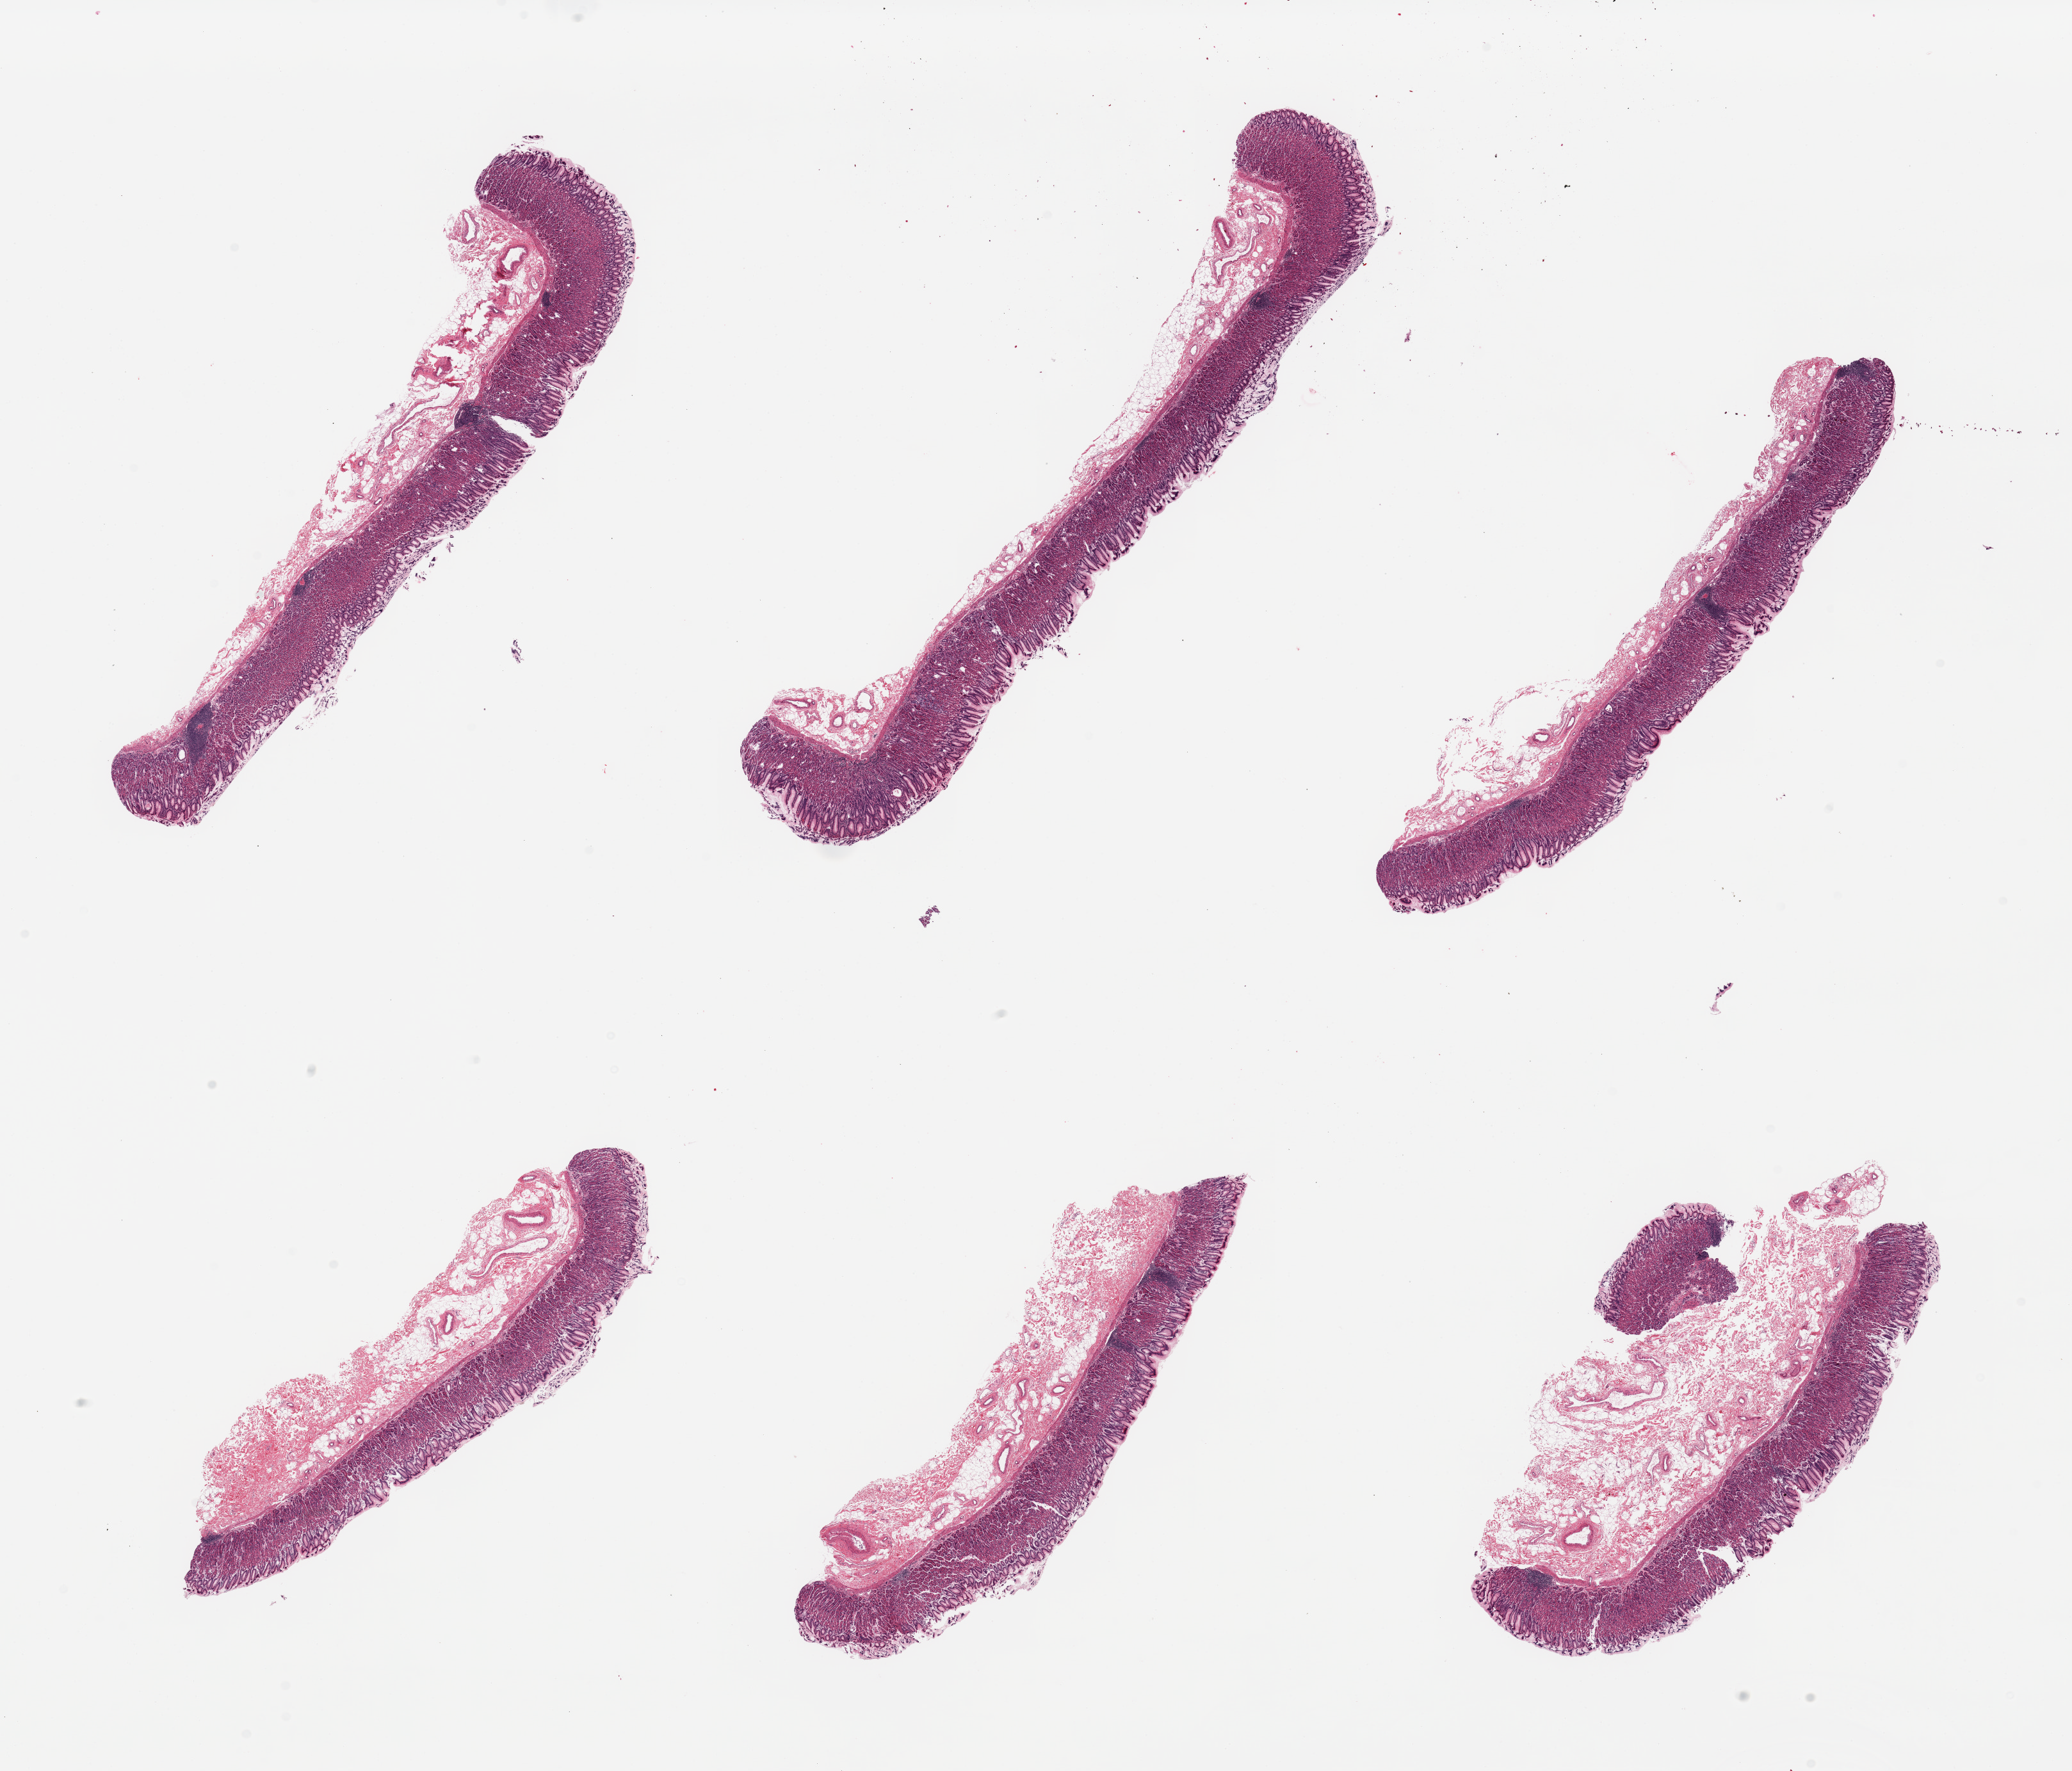
Digitized H&E-stained section, whole scanned area (about 25.6 x 21.9 mm) shown as a low-resolution overview, PAXgene-fixed paraffin-embedded (PFPE) section, section of stomach (target tissue), donor tissue sample. Donor: female.
Reviewer comment on this tissue sample: 6 pieces, mucosa well preserved, up to ~1mm thick, 50-100% thickness.